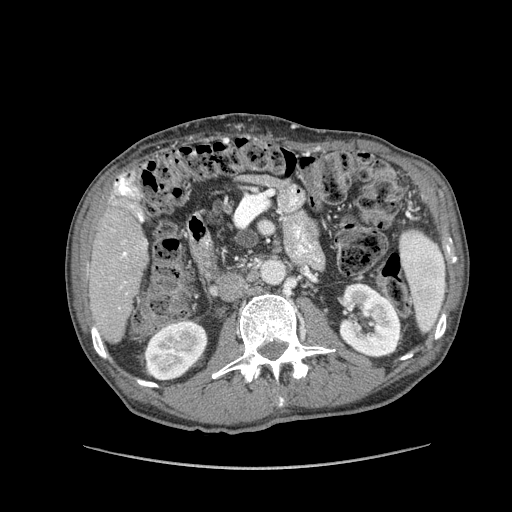
Contrast-enhanced abdominal CT (liver protocol), one axial slice; slice 31 of 162 in the series (ordered by position); soft-tissue window (W 400 / L 40 HU); 2.5 mm slice thickness; 512 × 512 image matrix. From the clinical record (not read from this slice): diagnosis: hepatocellular carcinoma (patient treated with transarterial chemoembolisation; whether this scan precedes or follows treatment is not stated here); TNM stage (as recorded): Stage-IIIA; Child-Pugh class: A; tumour nodularity: multinodular; tumour size: 9.9 cm.
Annotated regions visible in this slice (semi-automatic segmentation, software-assisted and operator-edited):
- liver parenchyma outside the tumour (the mass and vessels are separate outlines, so this box may not span the whole liver): bounding box [x1, y1, x2, y2] px = [86, 172, 148, 342]
- liver vessels: [115, 175, 146, 289]